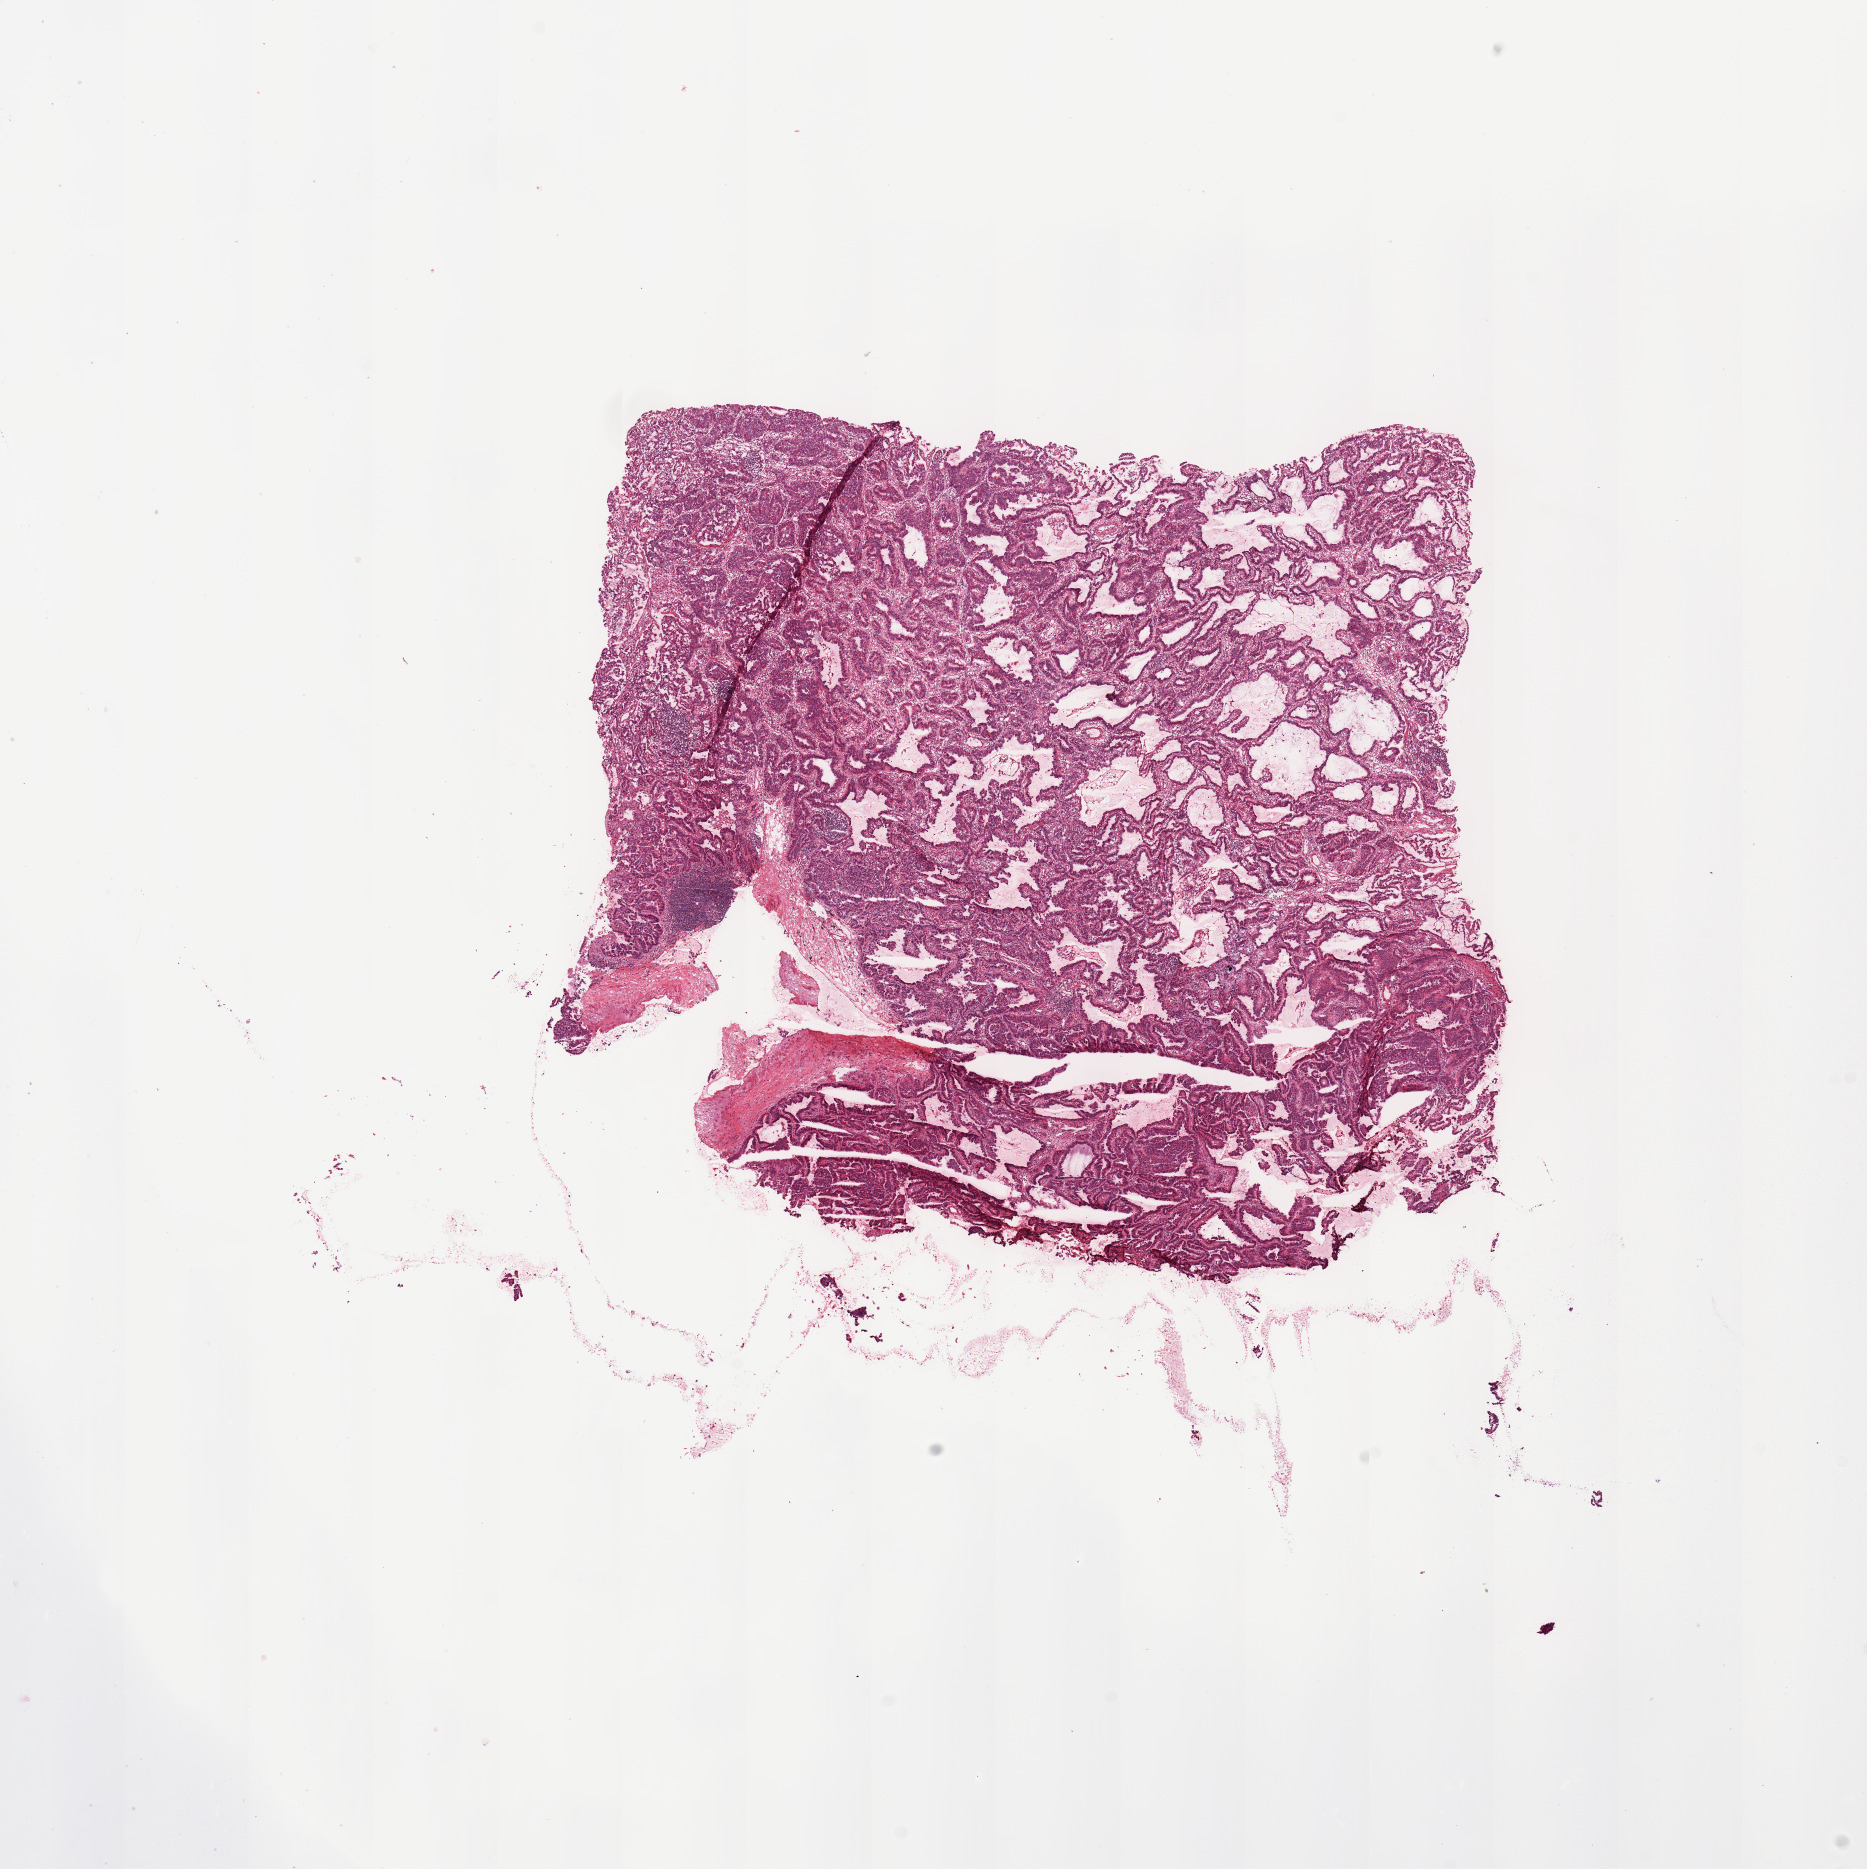
Whole-slide histology image, H&E-stained — whole scanned area (about 14.8 x 14.8 mm) shown as a low-resolution overview, tumour tissue sample, sampled site: lung. Female, 80 y/o.
Diagnosis: Adenocarcinoma, NOS.